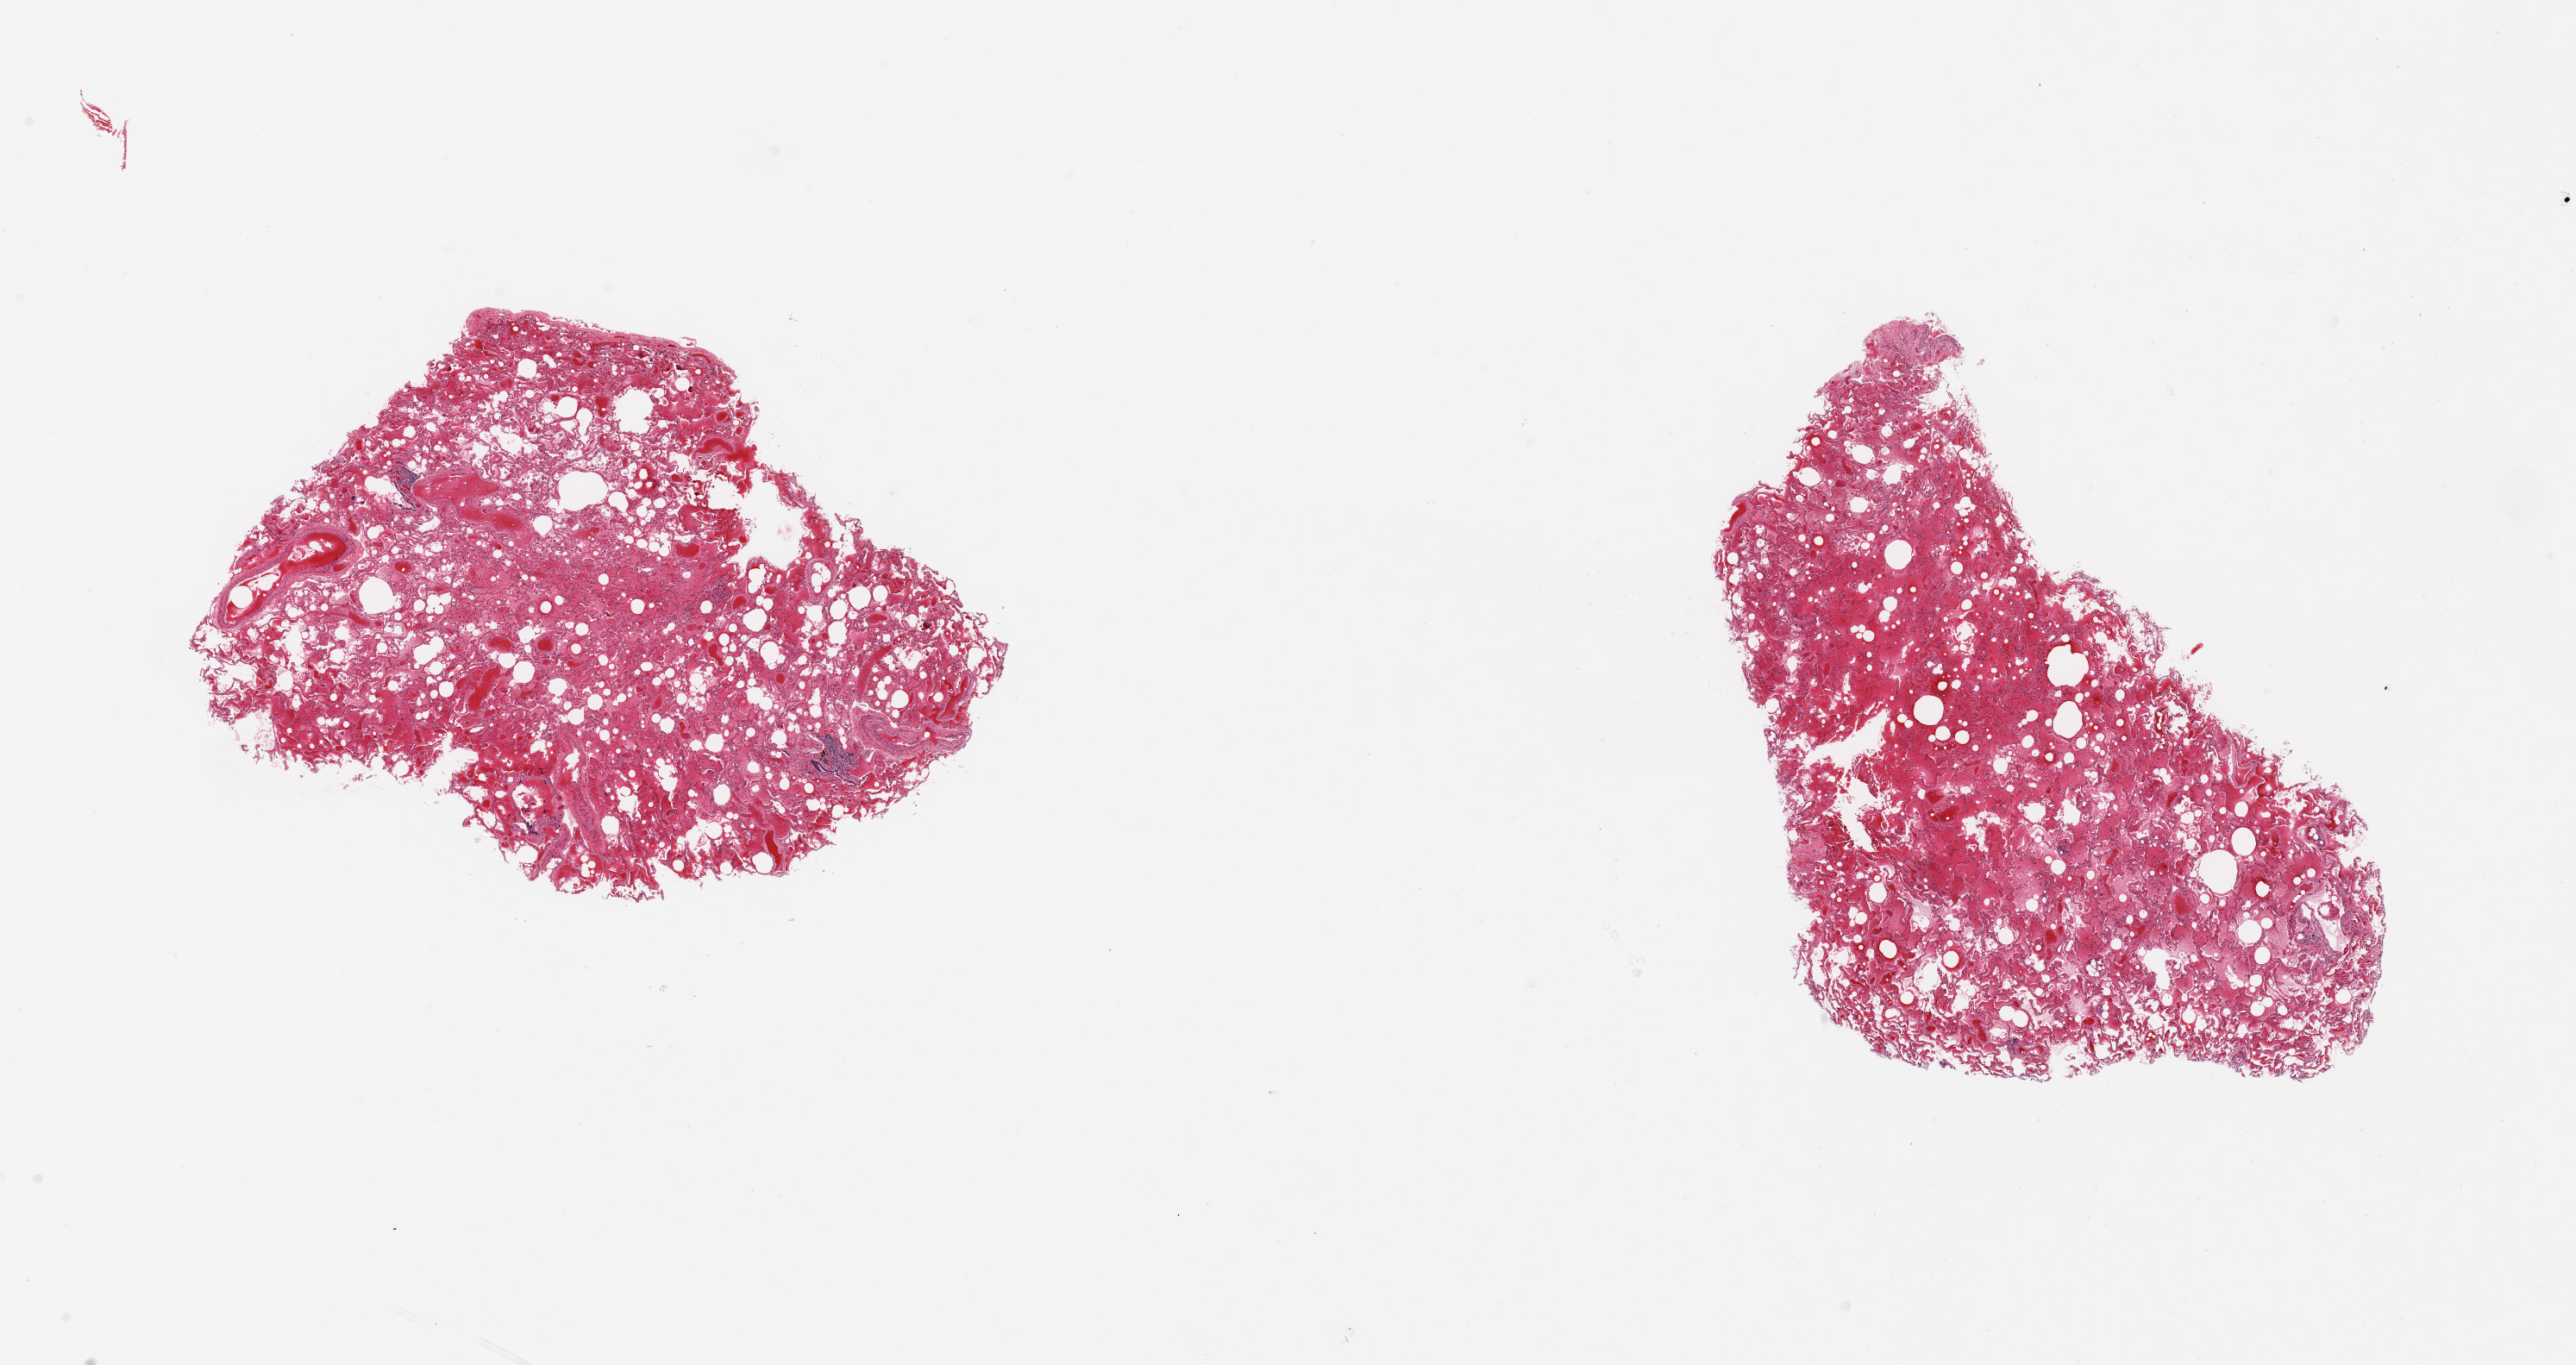
Haematoxylin and eosin whole-slide image, shown as a low-resolution overview of the whole scanned area (about 23.6 x 12.5 mm, from a 20x scan). PAXgene-fixed, paraffin-embedded tissue. Target tissue: lung. Tissue donor sample.
Reviewer comment on this tissue sample: 2 pieces; extensive alveolar hemorrhage.